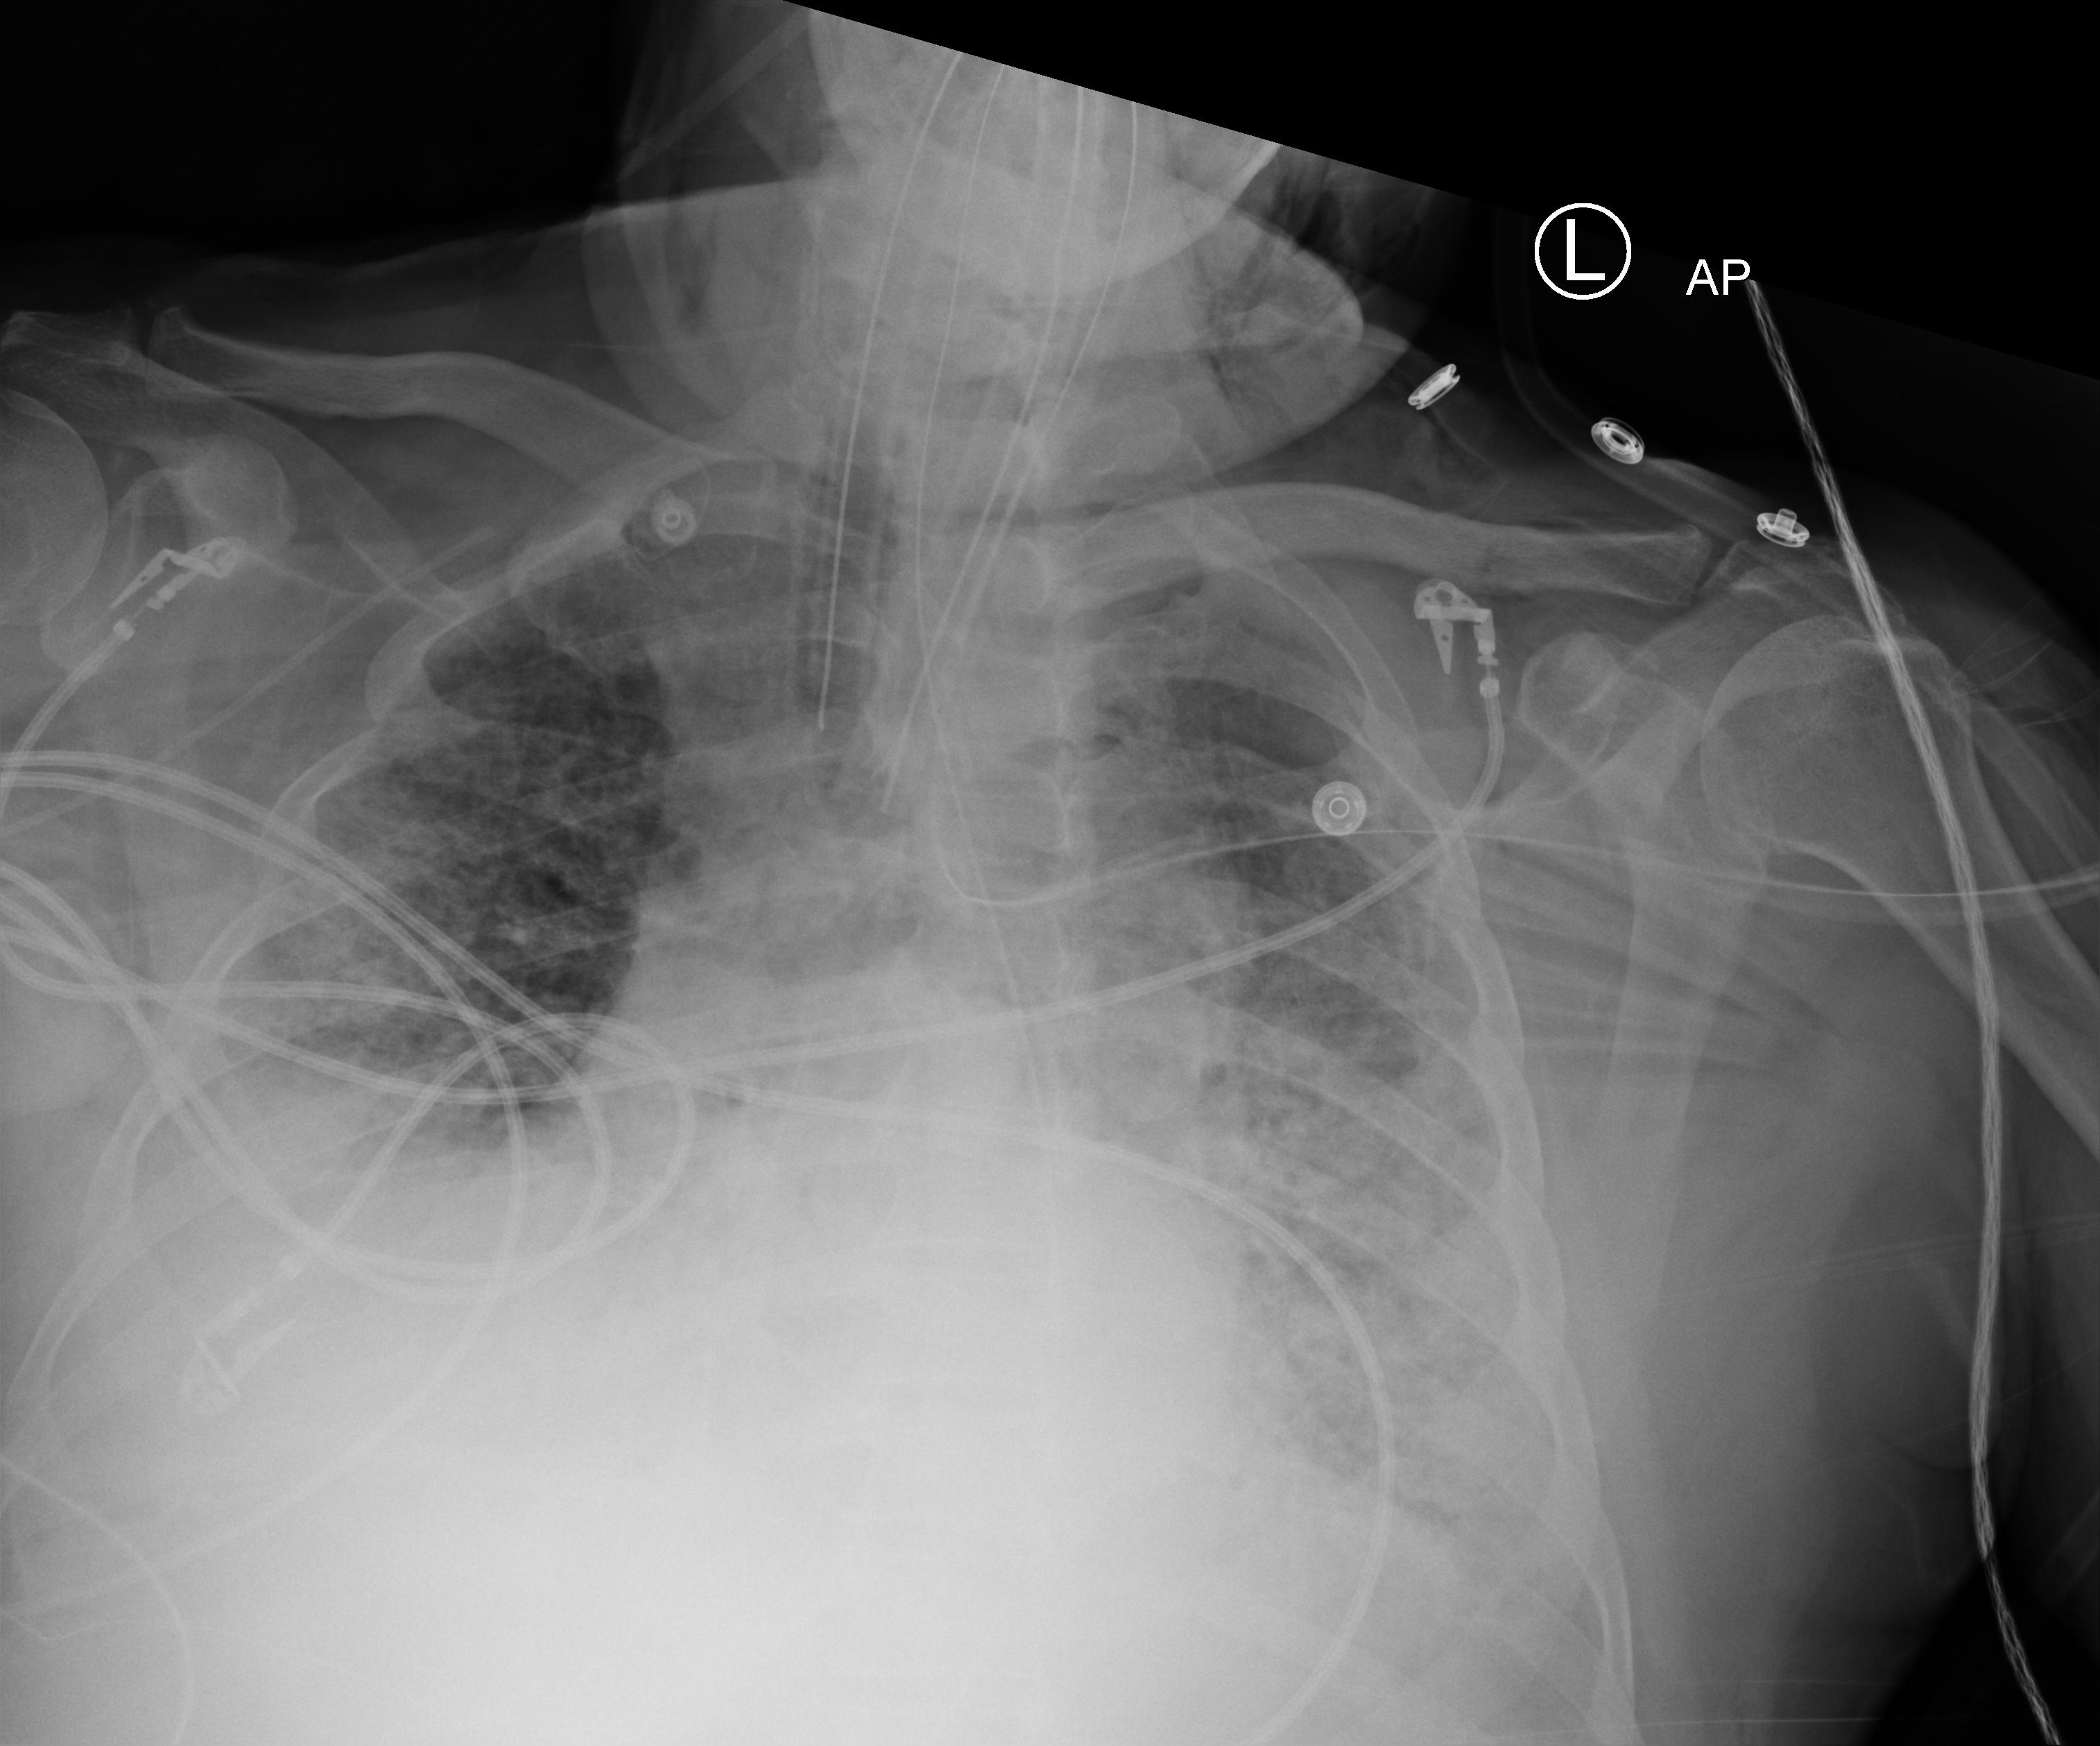
Bedside chest radiograph (computed radiography). Patient hospitalised with COVID-19; male, aged 60–74 years.
Hospital-stay facts (about this admission, not read from this image; timing relative to this image not recorded):
- length of hospital stay: 26 days
- mechanically ventilated during this hospital stay: yes
- admitted to intensive care during this hospital stay: yes